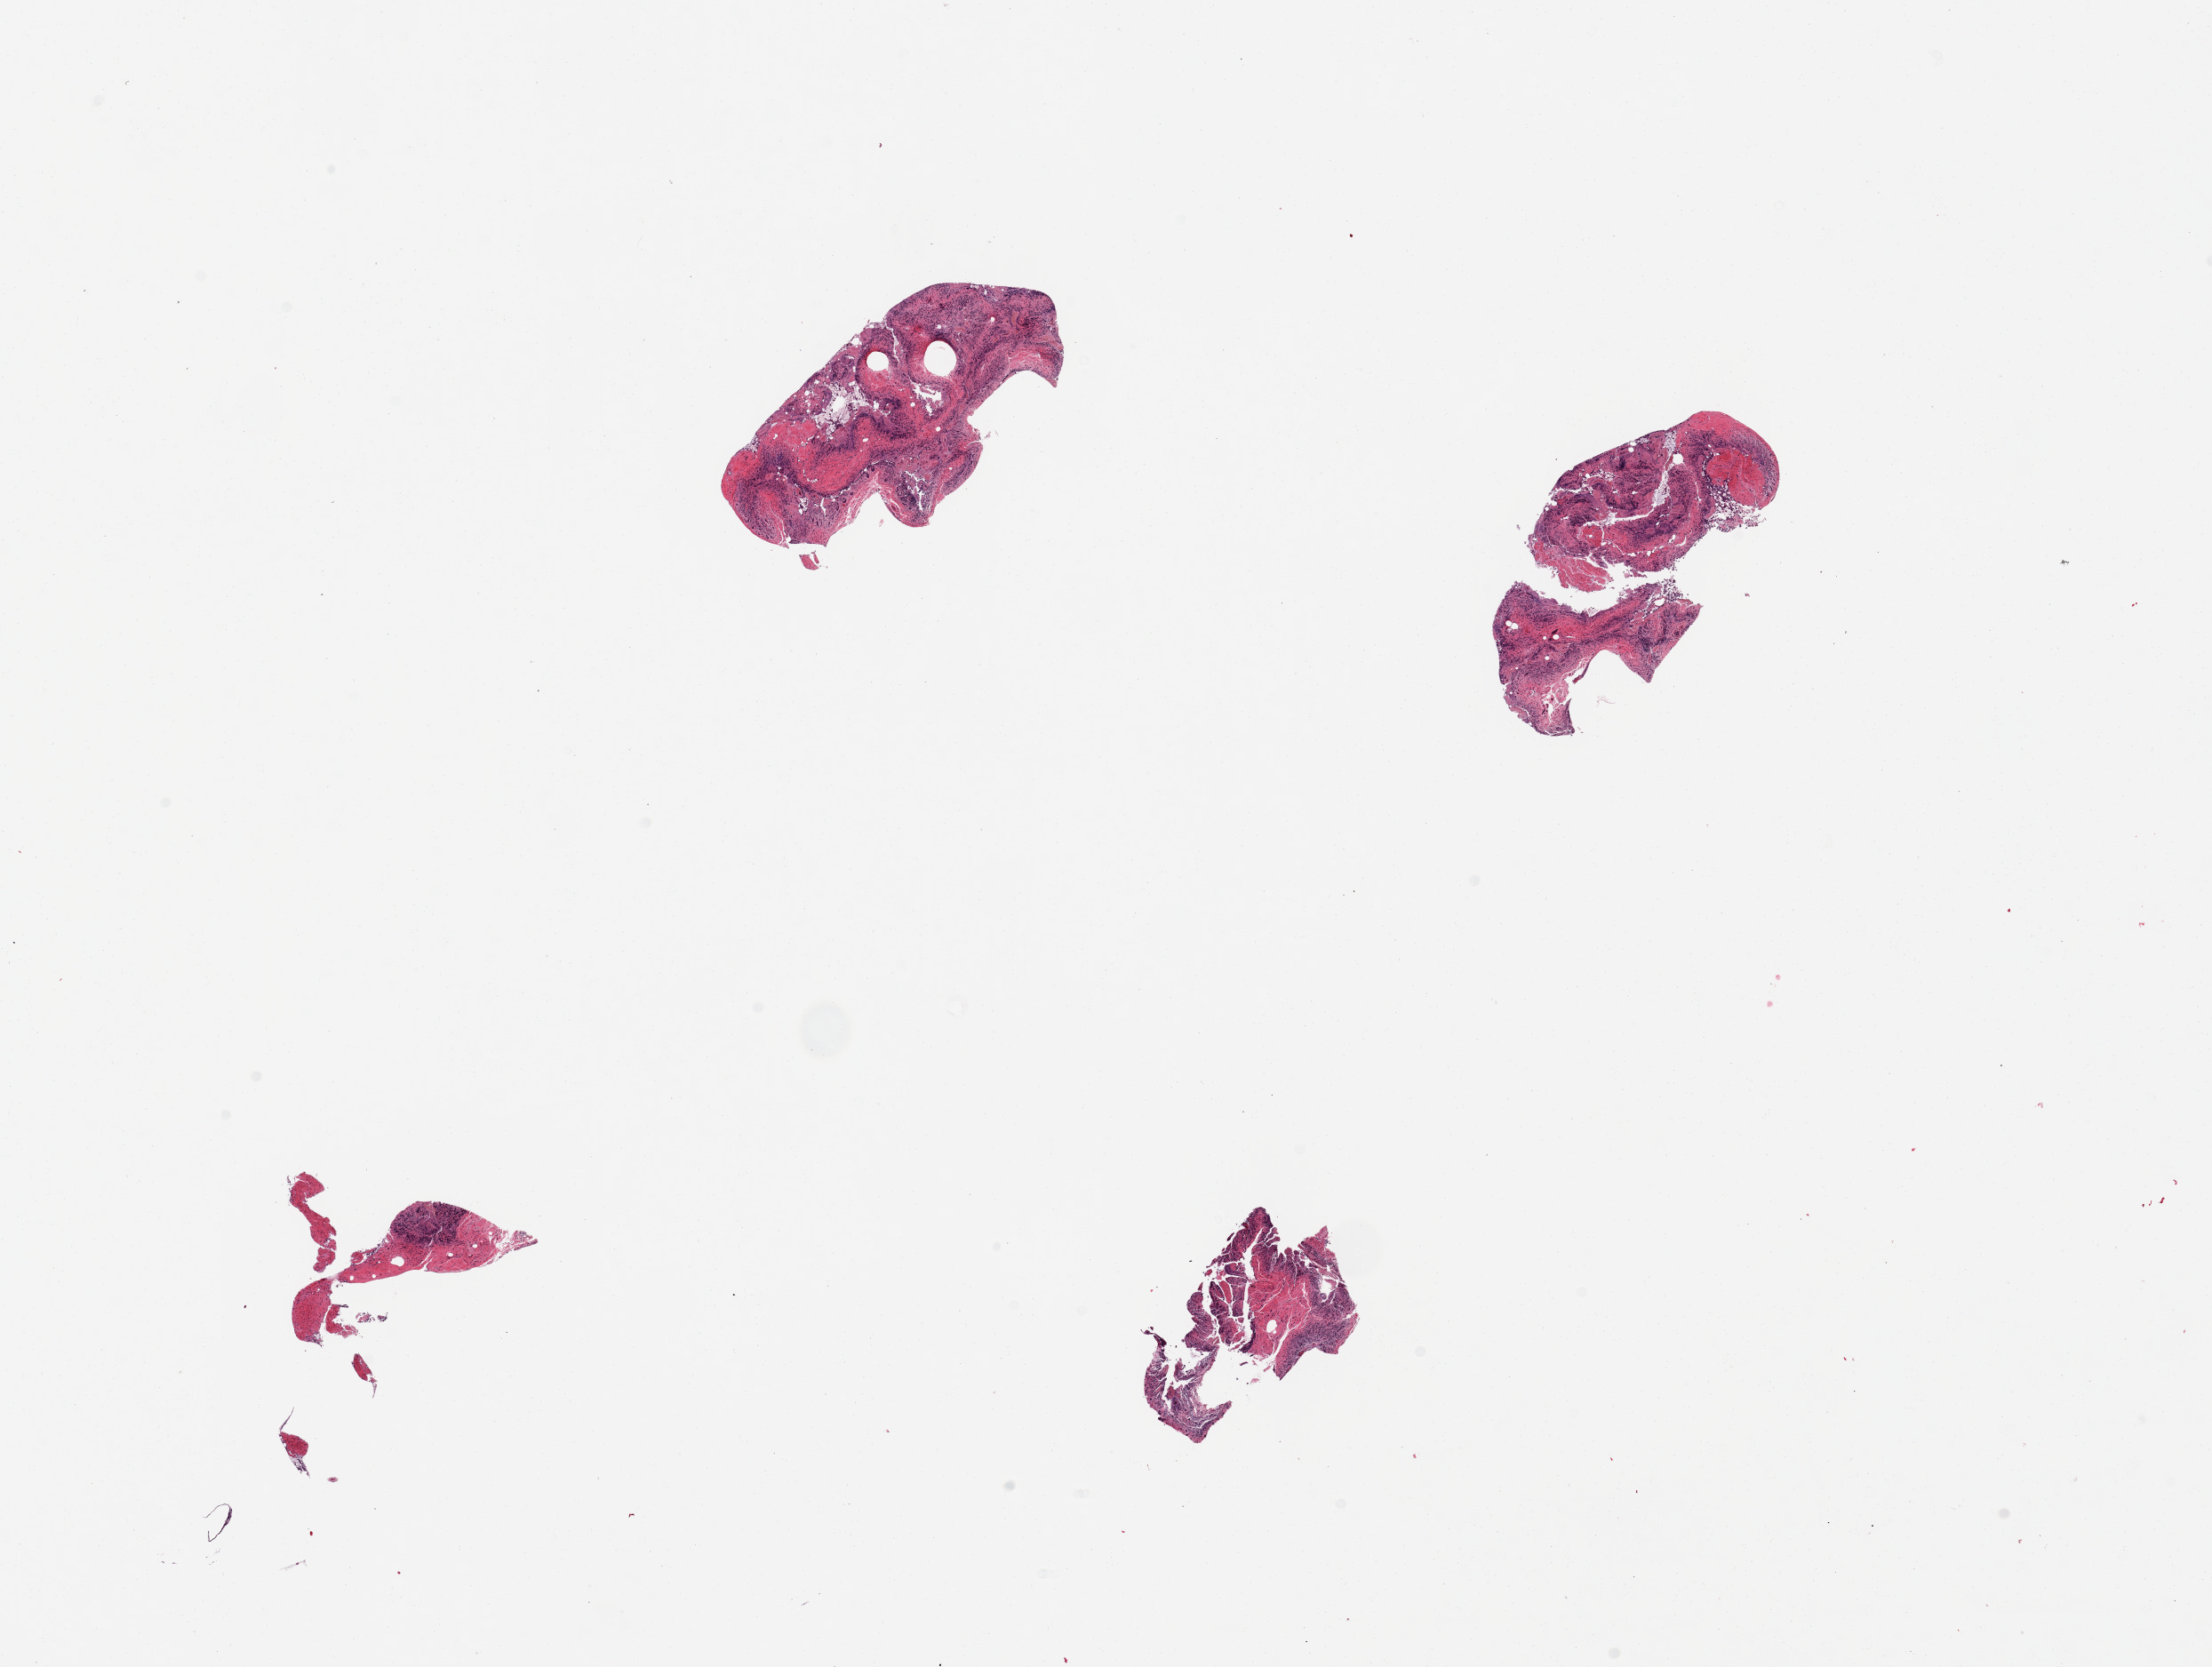
Hematoxylin and eosin (H&E) whole-slide image, brightfield — low-resolution overview of the scanned area, about 19.7 x 14.8 mm; PAXgene-fixed, paraffin-embedded tissue; target tissue: ileum; tissue donor sample. Male donor.
• pathologist's review note for this sample: 4 pieces; autolyzed mucosa and paucity of lymphoid nodules